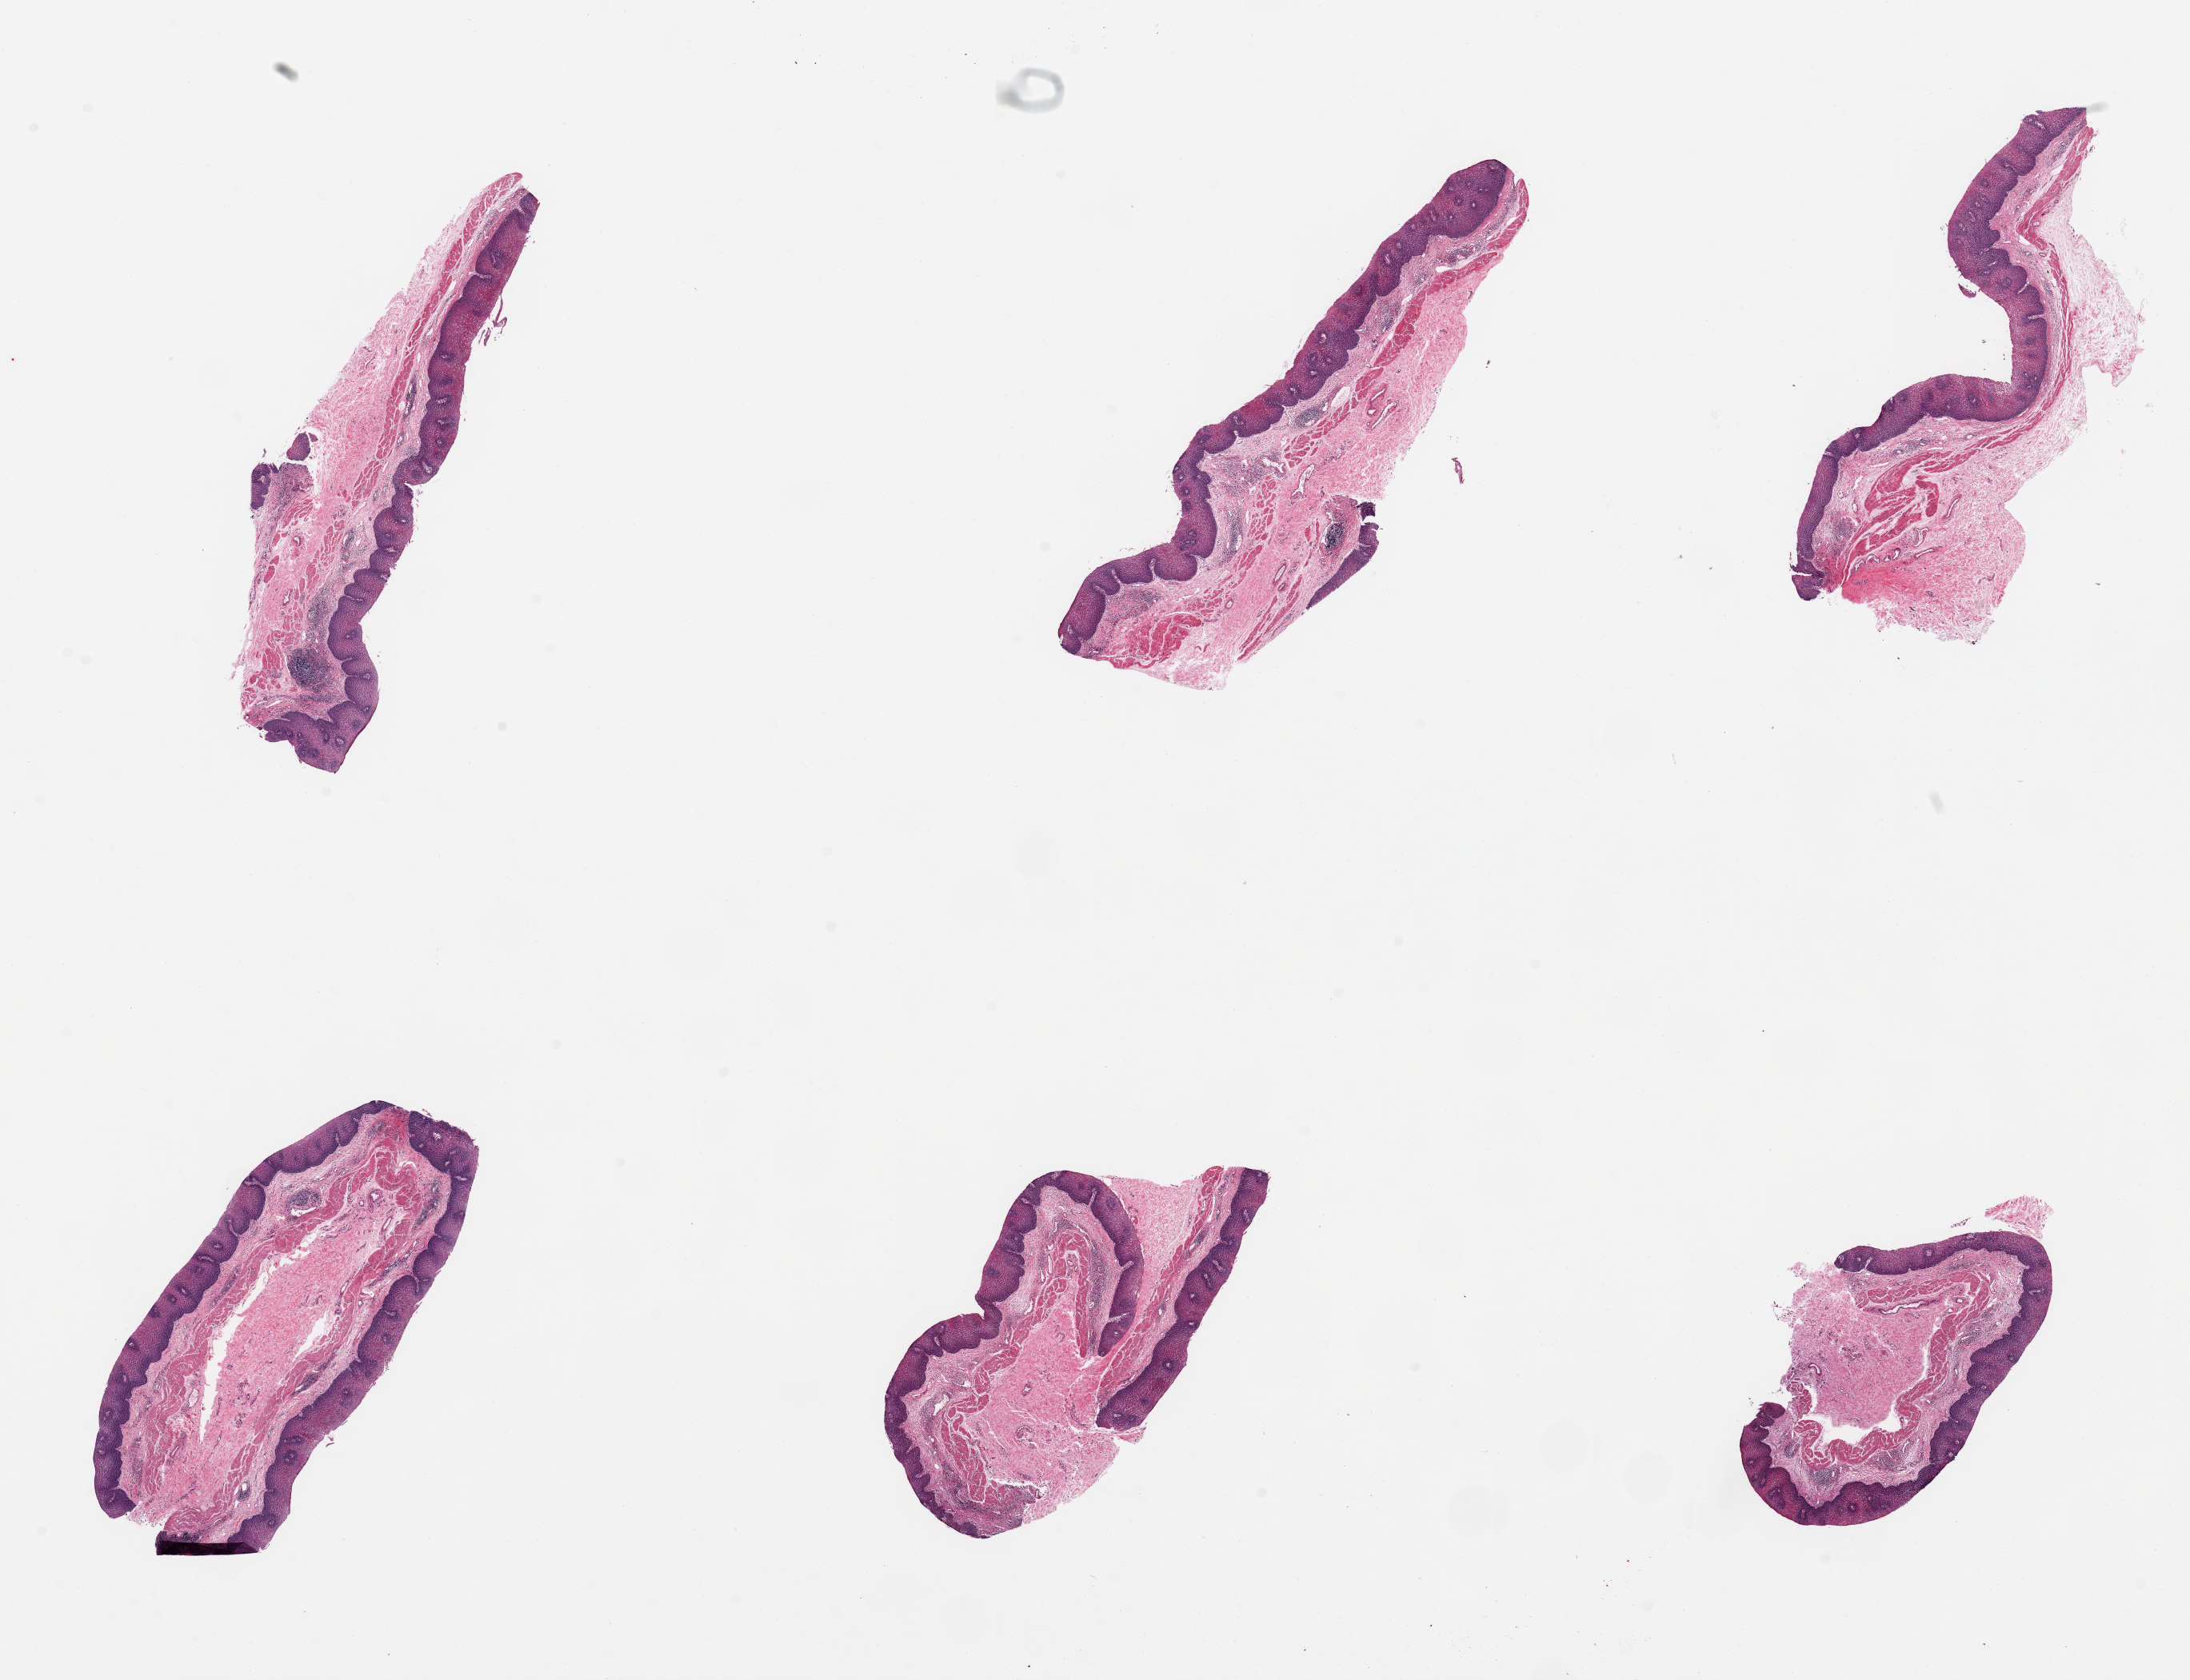
Whole-slide image, H&E stain — shown as a low-resolution overview of the whole scanned area (about 21.7 x 16.6 mm). PAXgene-fixed paraffin-embedded (PFPE) section. Sampled site (target tissue): esophageal mucous membrane. Donor tissue sample. Donor: male.
Reviewer comment on this tissue sample: 6 pieces; moderate chronic esophagitis (focal lymphoid deposits in lamina propria).